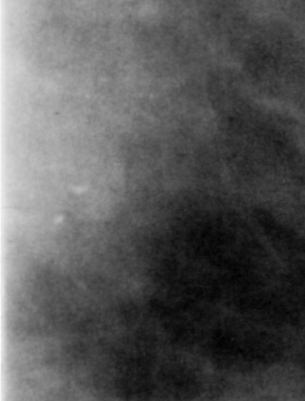
Crop from a digitized film mammogram around one marked abnormality; right breast; MLO view; BI-RADS breast density category 4 (scale 1–4).
- Calcifications, morphology pleomorphic, distribution clustered; BI-RADS assessment category 4; subtlety rating 3 on a 1 (subtle) to 5 (obvious) scale; pathology (as recorded): benign.